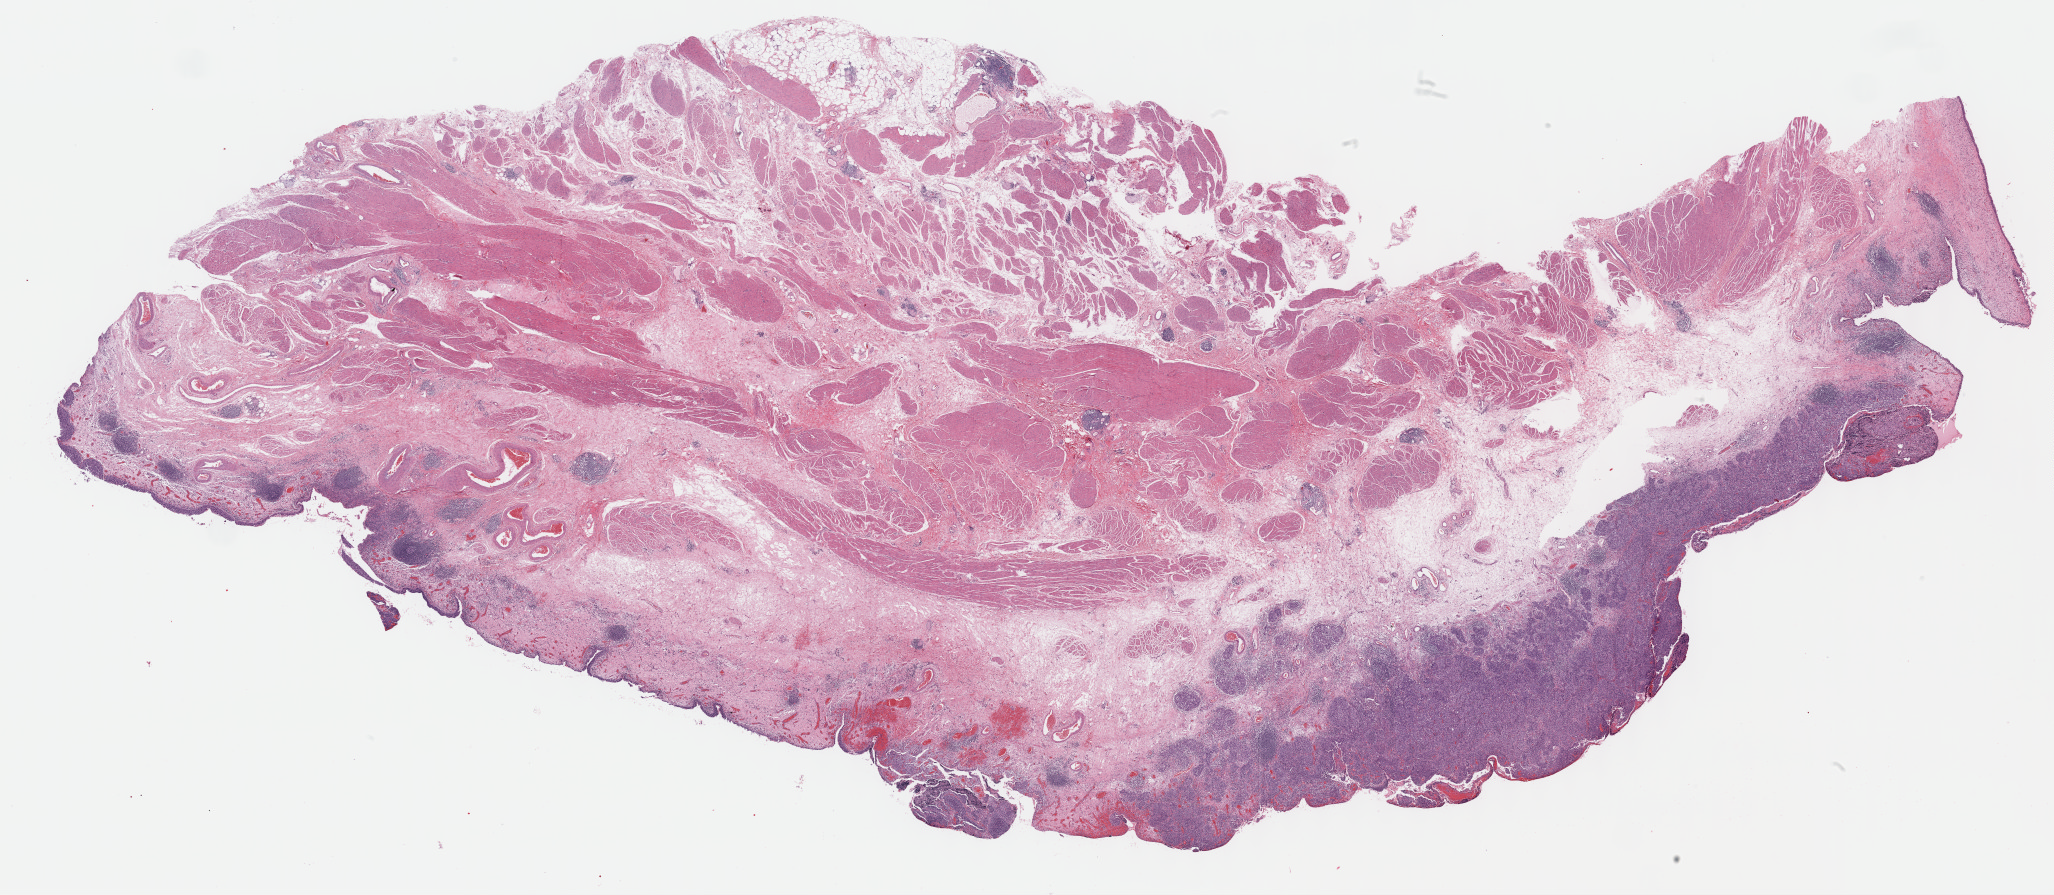
H&E-stained whole-slide image — whole scanned area (about 33.2 x 14.5 mm) shown as a low-resolution overview. FFPE section. Primary tumour sample from the bladder. Female patient; age at initial diagnosis 87 years.
Histologic diagnosis: Transitional cell carcinoma.